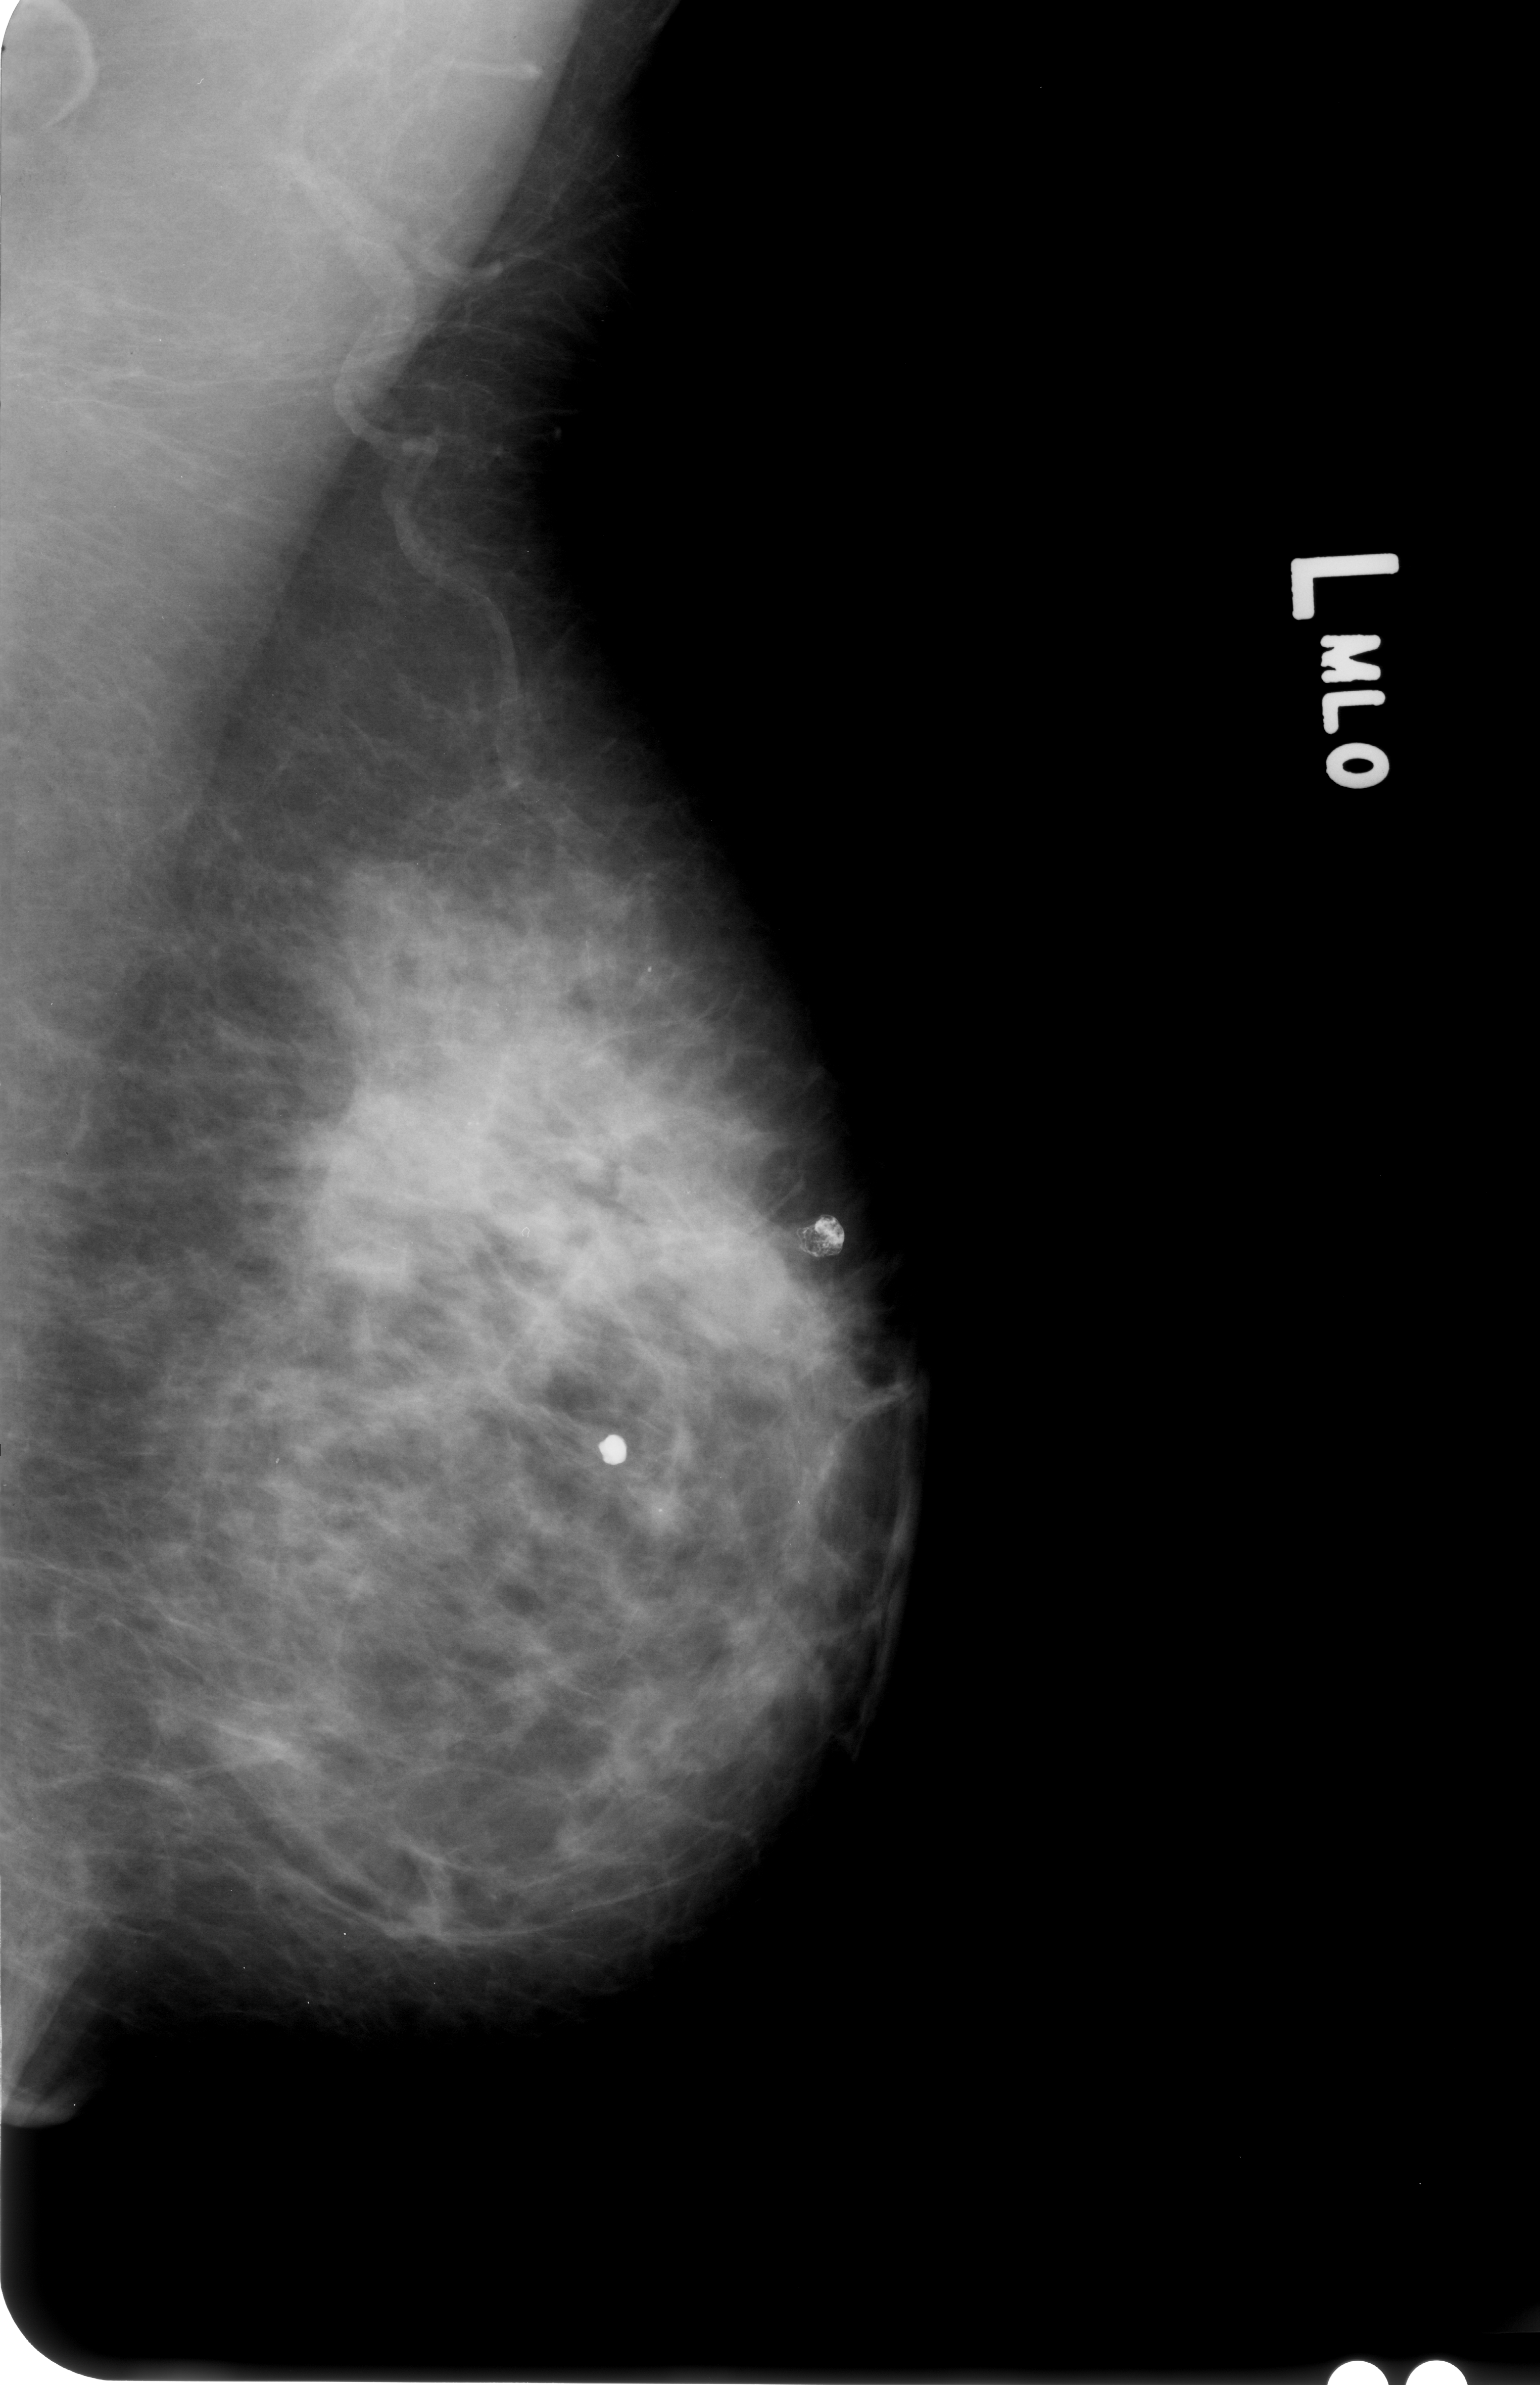
Mammogram (digitized film); left breast; mediolateral oblique (MLO) view; BI-RADS breast density category 3 (scale 1–4).
Calcifications, morphology punctate, distribution segmental; BI-RADS assessment category 4; pathology (as recorded): malignant.